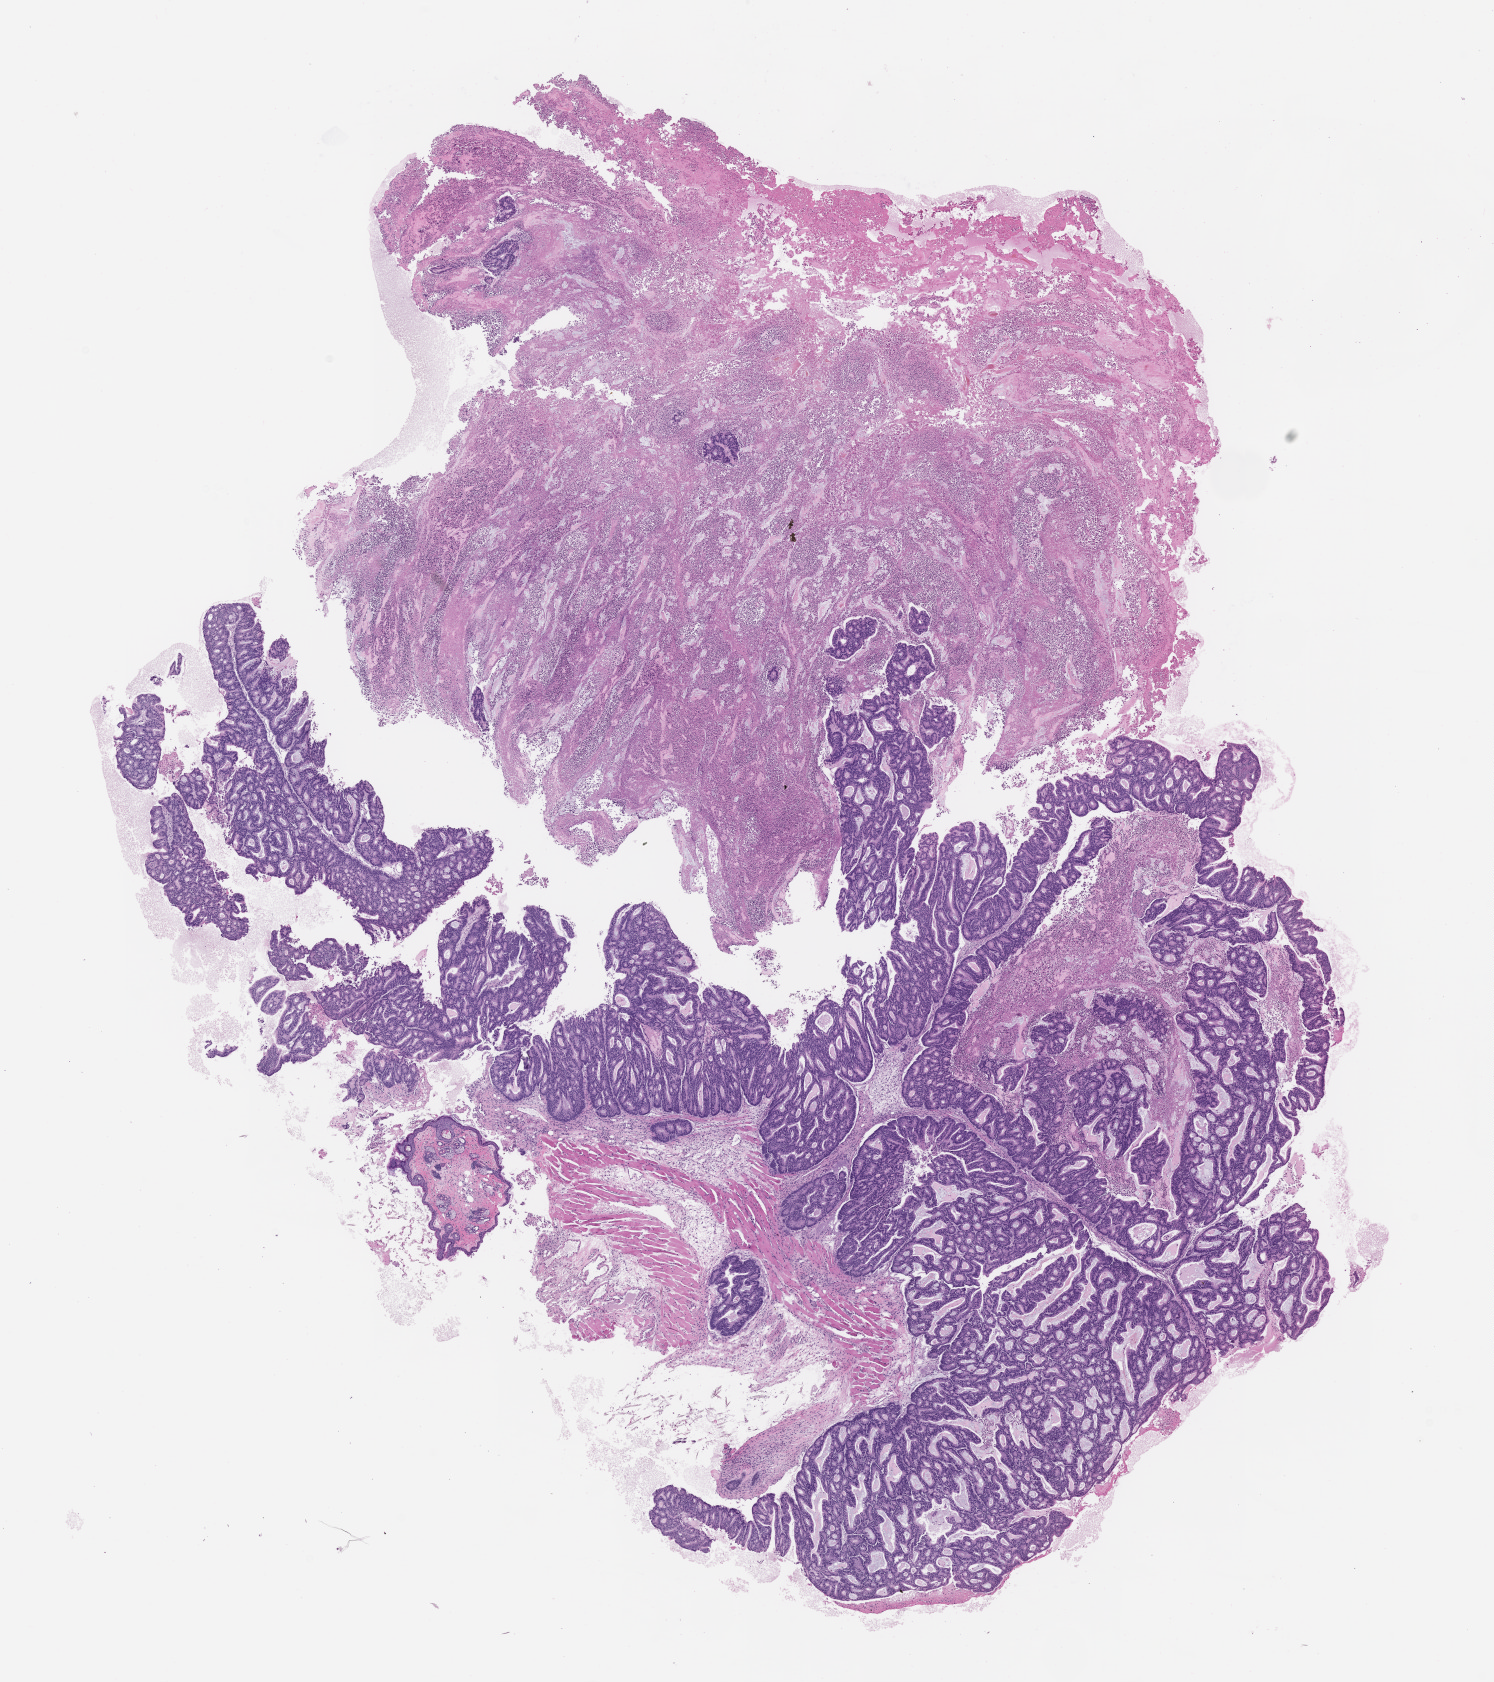
Whole-slide image, hematoxylin and eosin (H&E): patient-derived xenograft (human tumor grown in a mouse), passage 6, shown as a low-resolution overview of the whole scanned area (about 12.0 x 13.5 mm); formalin-fixed paraffin-embedded section; originating tumor site category: colon.
- originating patient diagnosis: Colon Adenocarcinoma